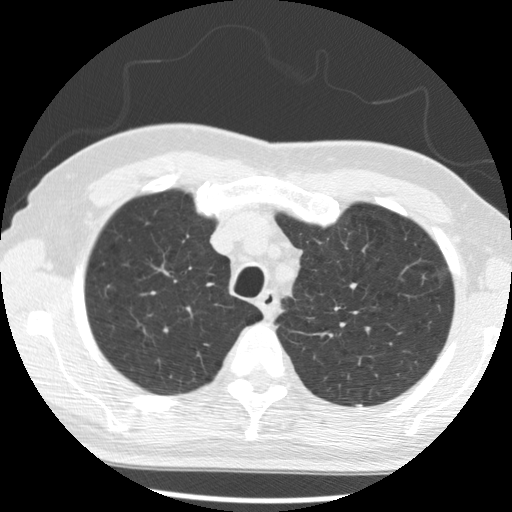
Low-dose screening chest CT, axial slice, second annual screen, lung window (W 1500 / L -600 HU), 512 × 512 image matrix, field of view 340 × 340 mm. Male participant, aged 68 years at enrolment. Current smoker at enrolment.
Expert-annotated lung lesion, bounding box [x1, y1, x2, y2] px = [420, 262, 461, 294]. Reader record for this screening exam (exam-level; its link to the box is not recorded): non-calcified nodule or mass ≥4 mm, left upper lobe, 15 × 11 mm, poorly defined margins, ground glass attenuation, pre-existing on the prior screen: yes; interval growth: yes. Official screen result: positive, change unspecified: nodule(s) >= 4 mm or enlarging nodule(s), mass(es), or other non-specific abnormalities suspicious for lung cancer.